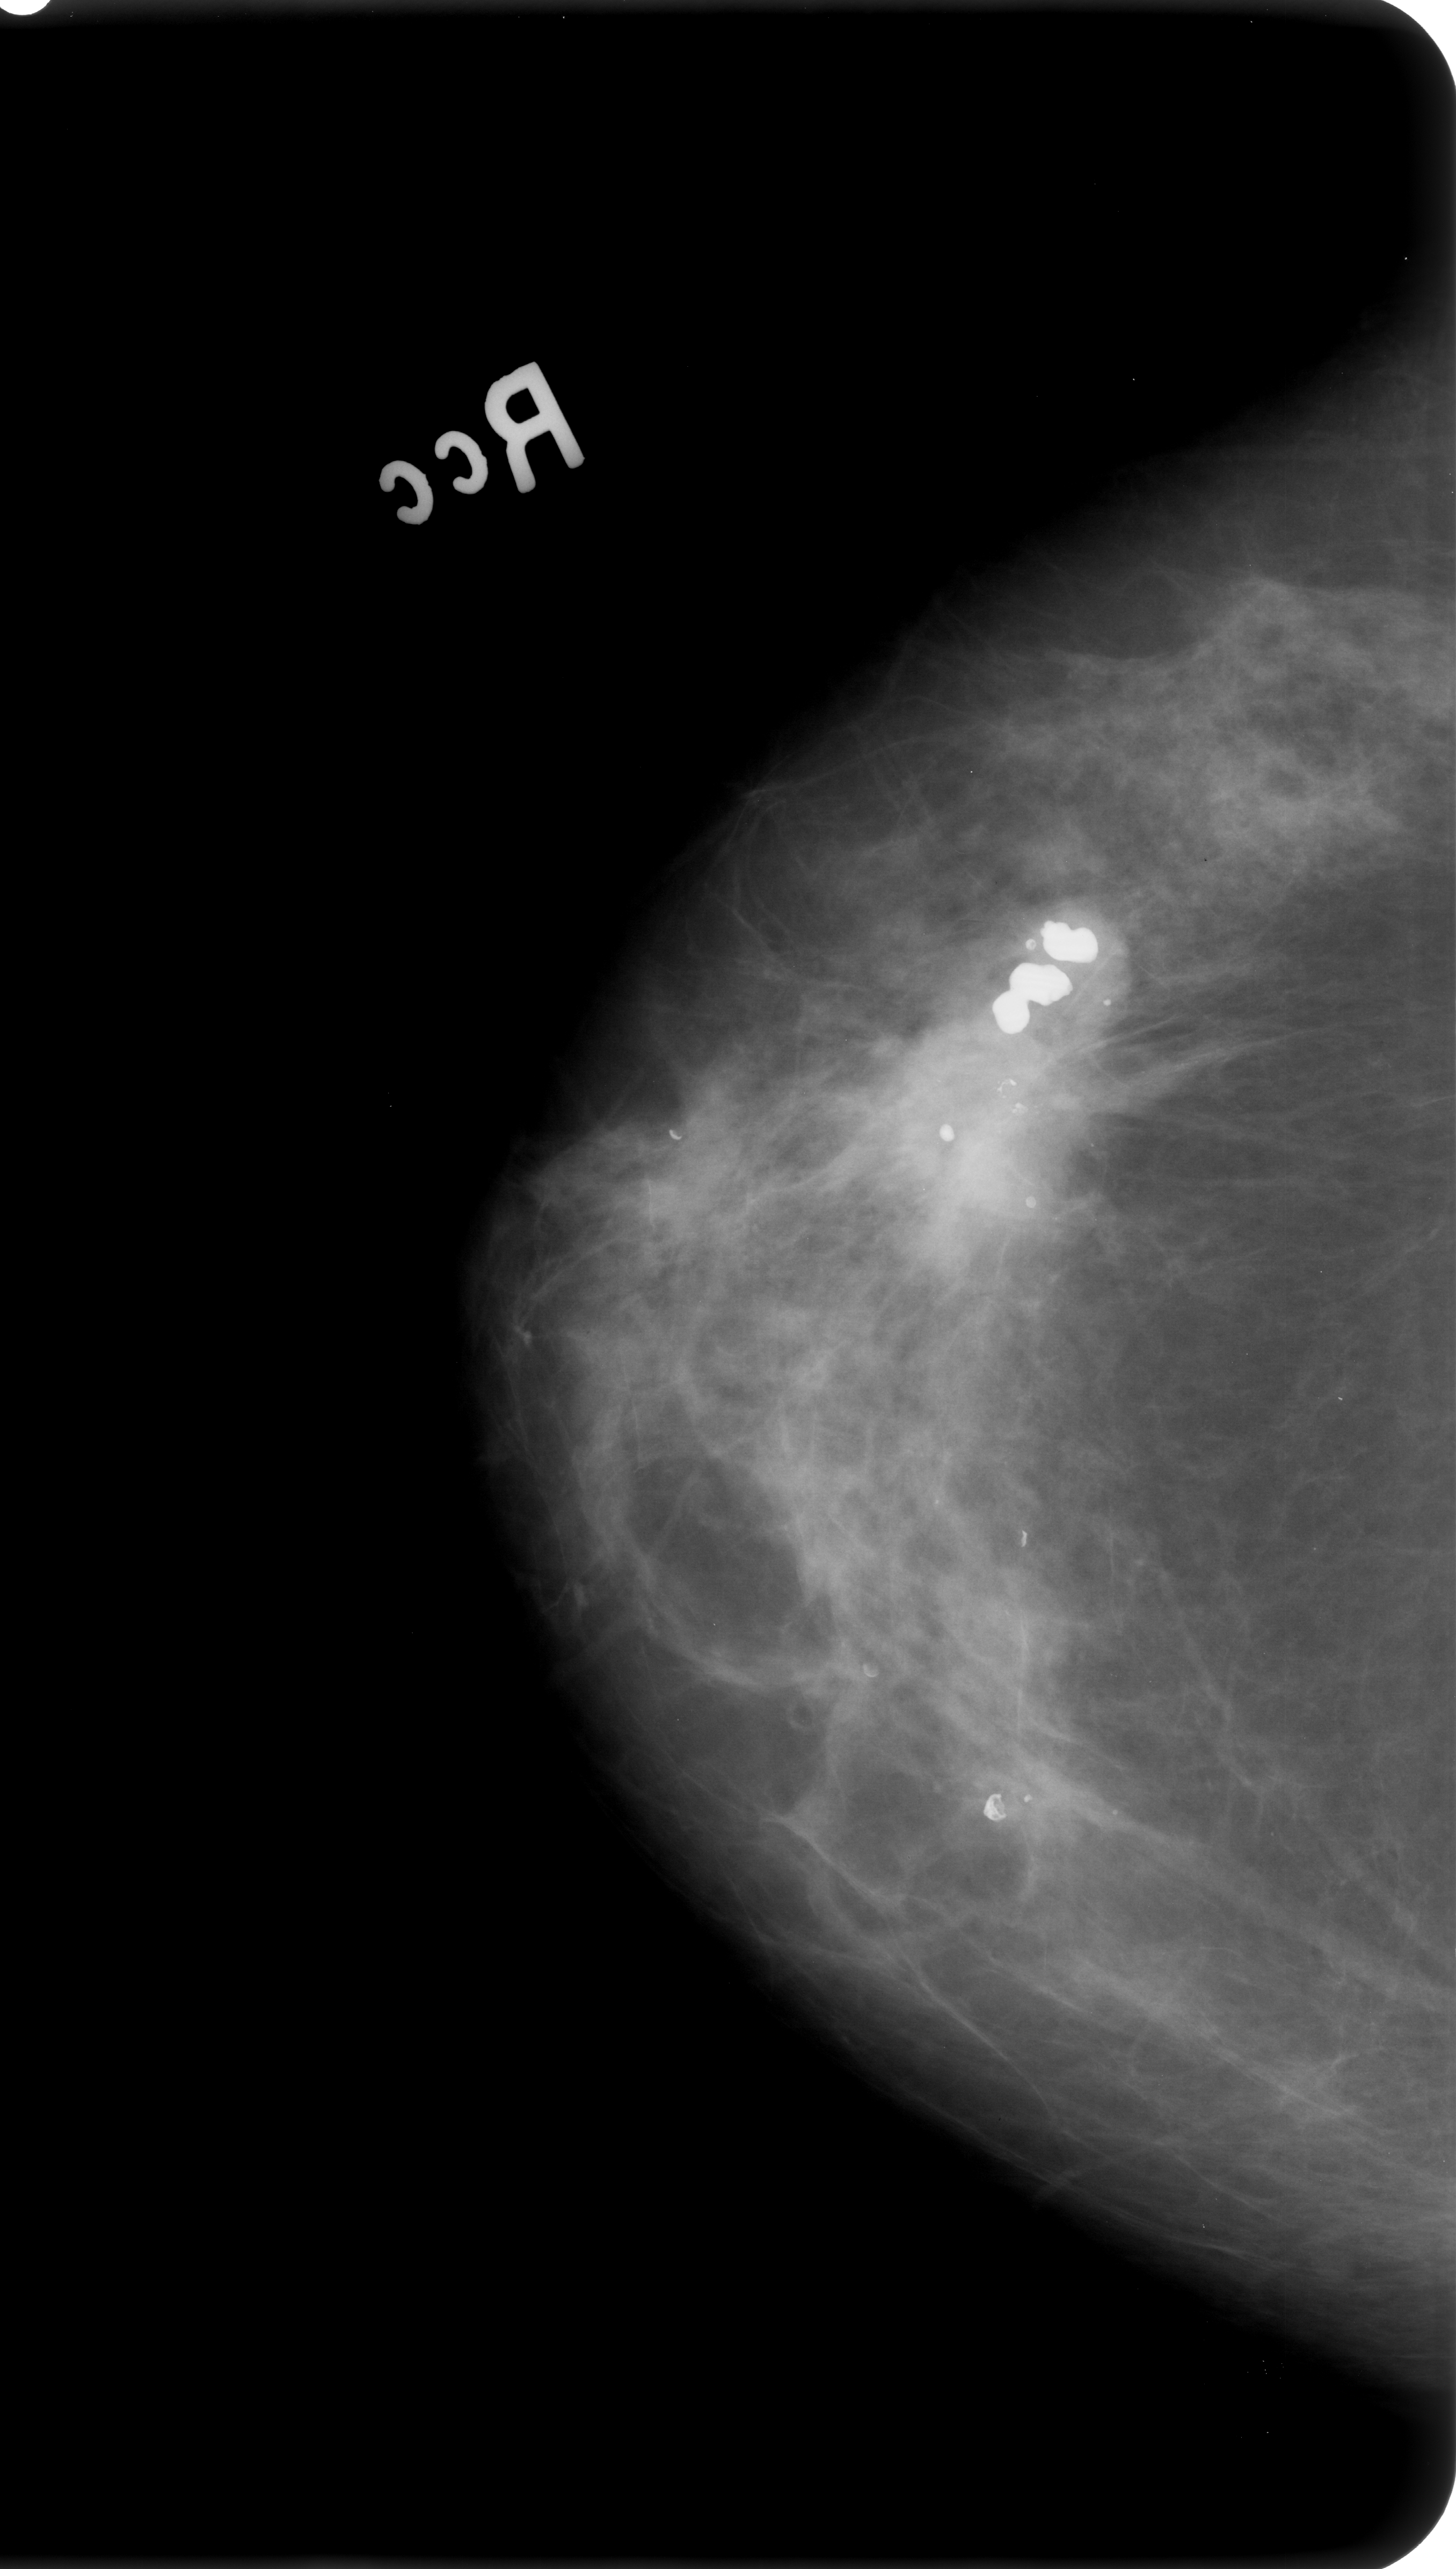
Scanned film-screen mammogram, right breast, CC view, breast composition: heterogeneously dense (BI-RADS density category 3 of 4).
Finding: mass, shape architectural distortion, margins spiculated; BI-RADS assessment category 4; pathology result (as recorded, not read from the image): malignant.